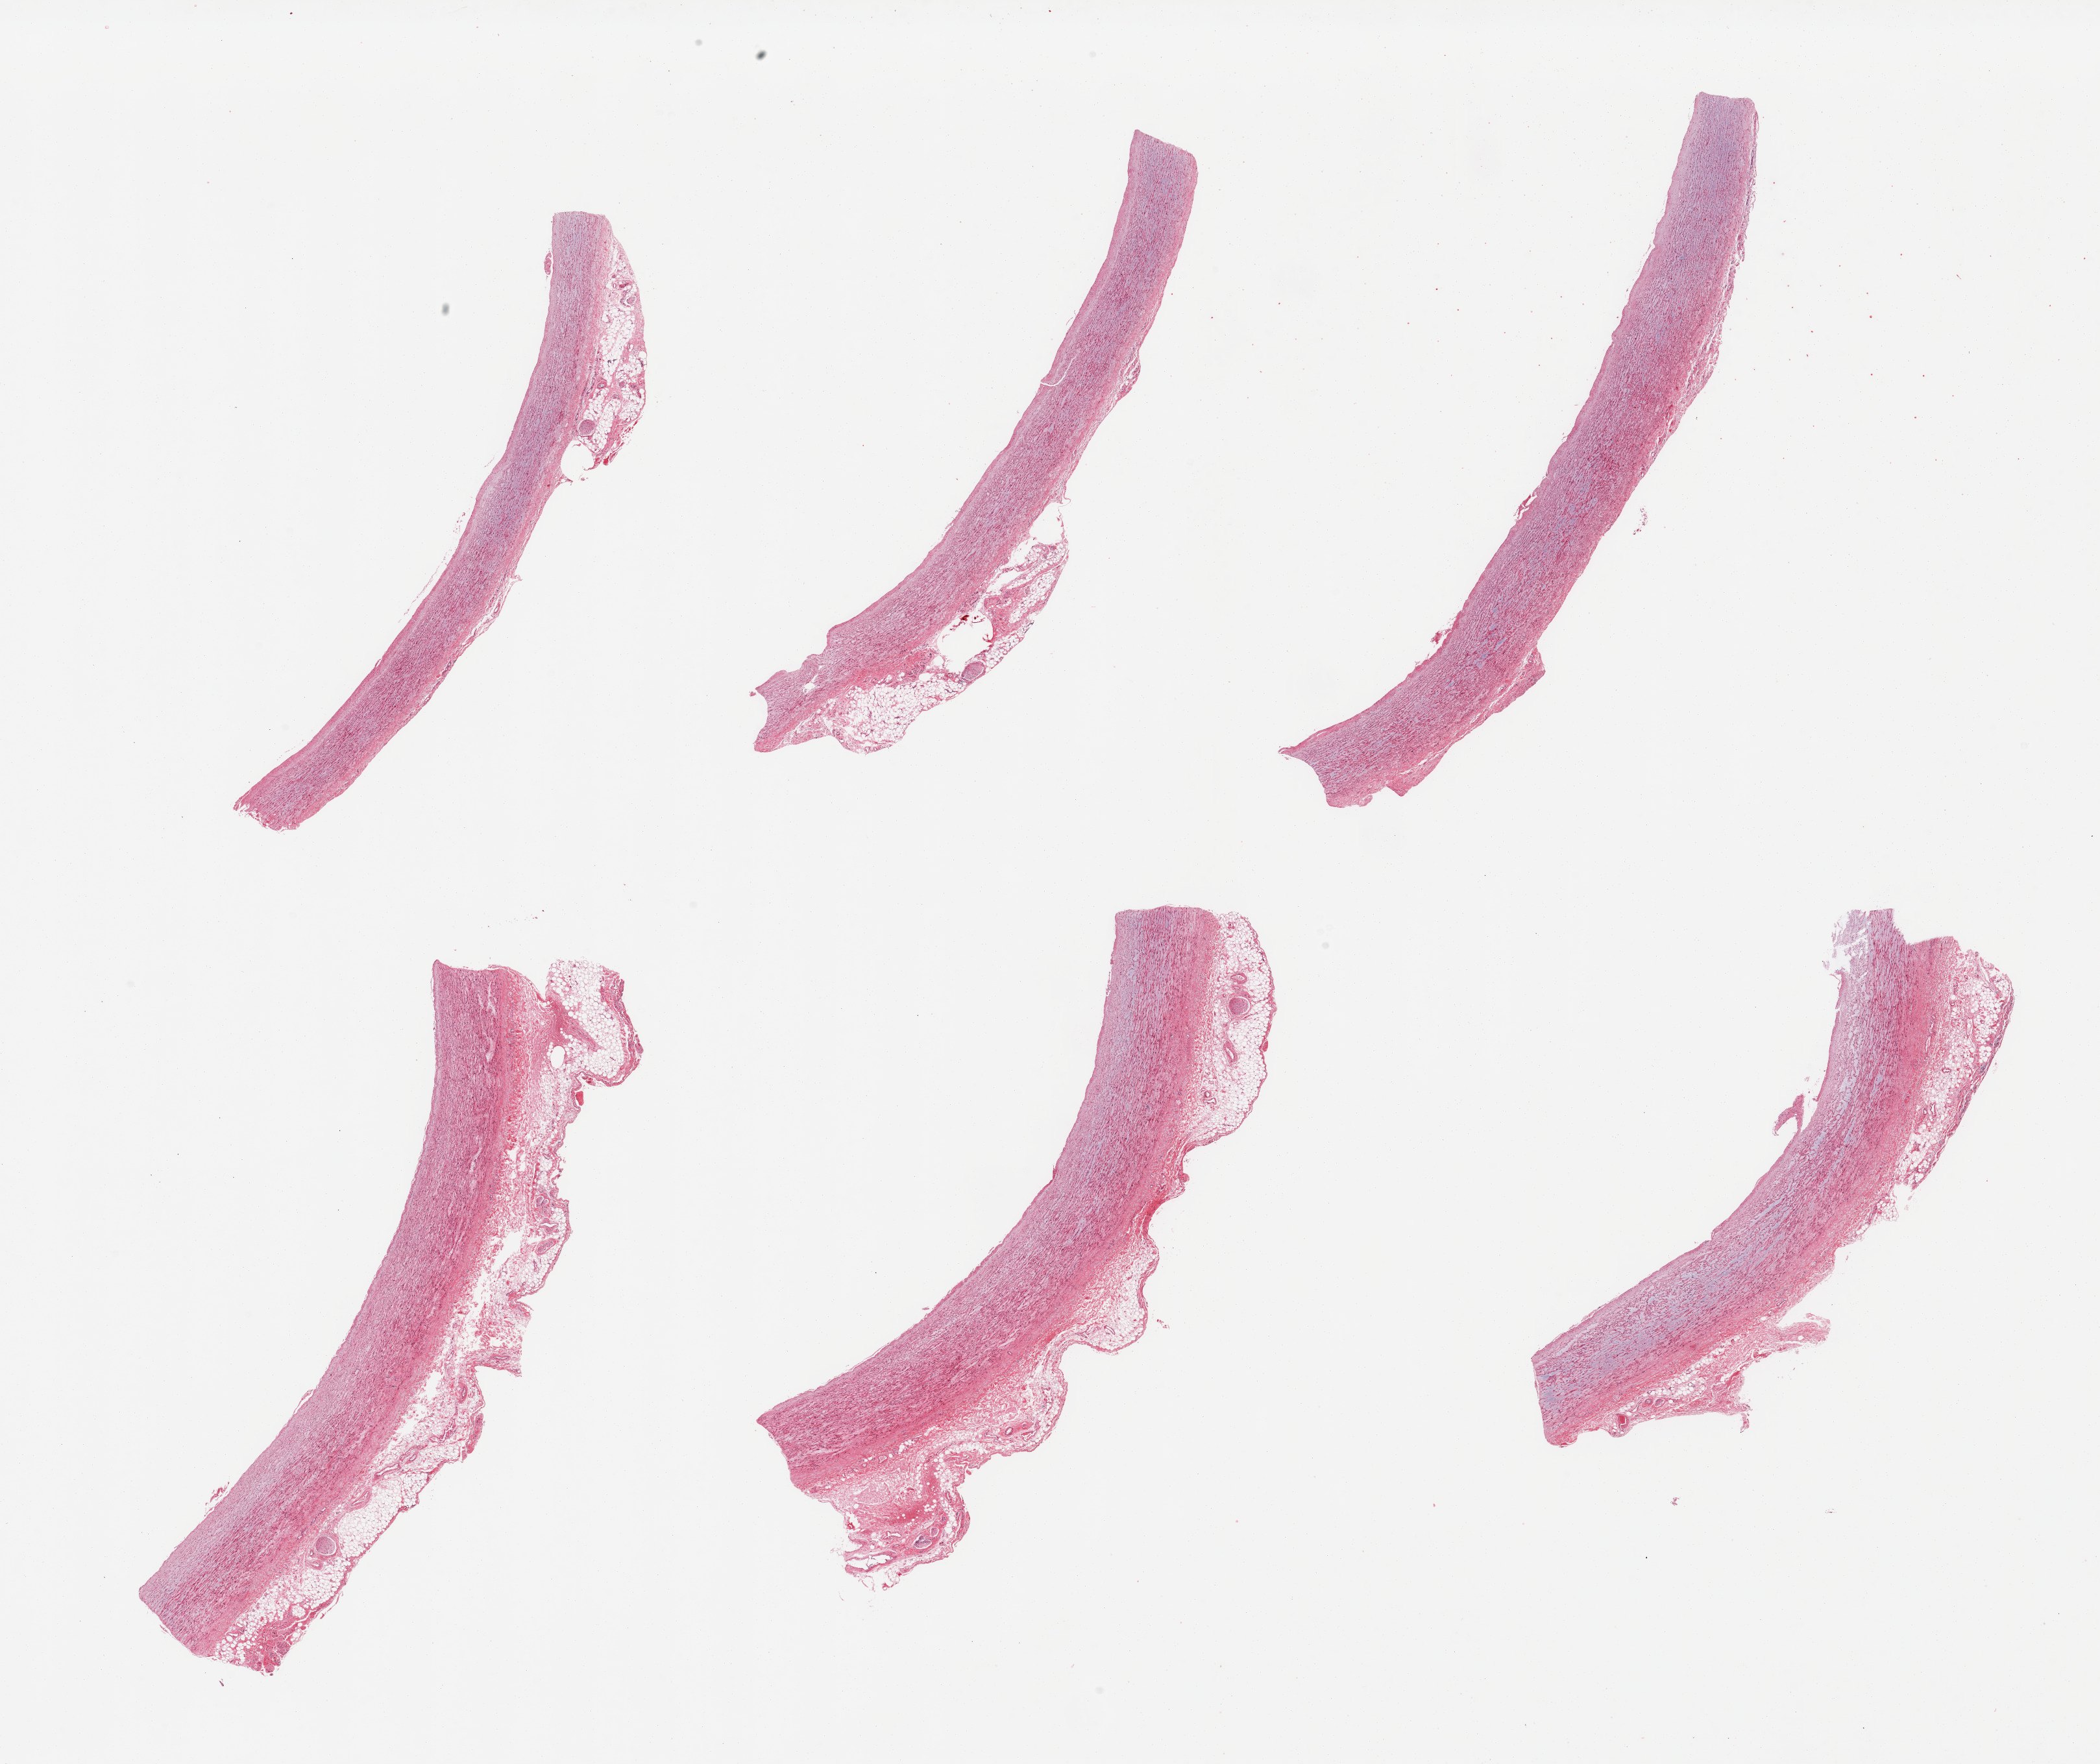
Whole-slide image, hematoxylin and eosin (H&E) stain — whole scanned area (about 25.6 x 21.5 mm) shown as a low-resolution overview, PAXgene-fixed paraffin-embedded (PFPE) section, target tissue: auricular appendage, tissue donor sample. Donor: female.
Reviewer comment on this tissue sample: 6 pieces; NOT atrial appendage; aorta with interstitial myxoid degeneration; no significant plaque.